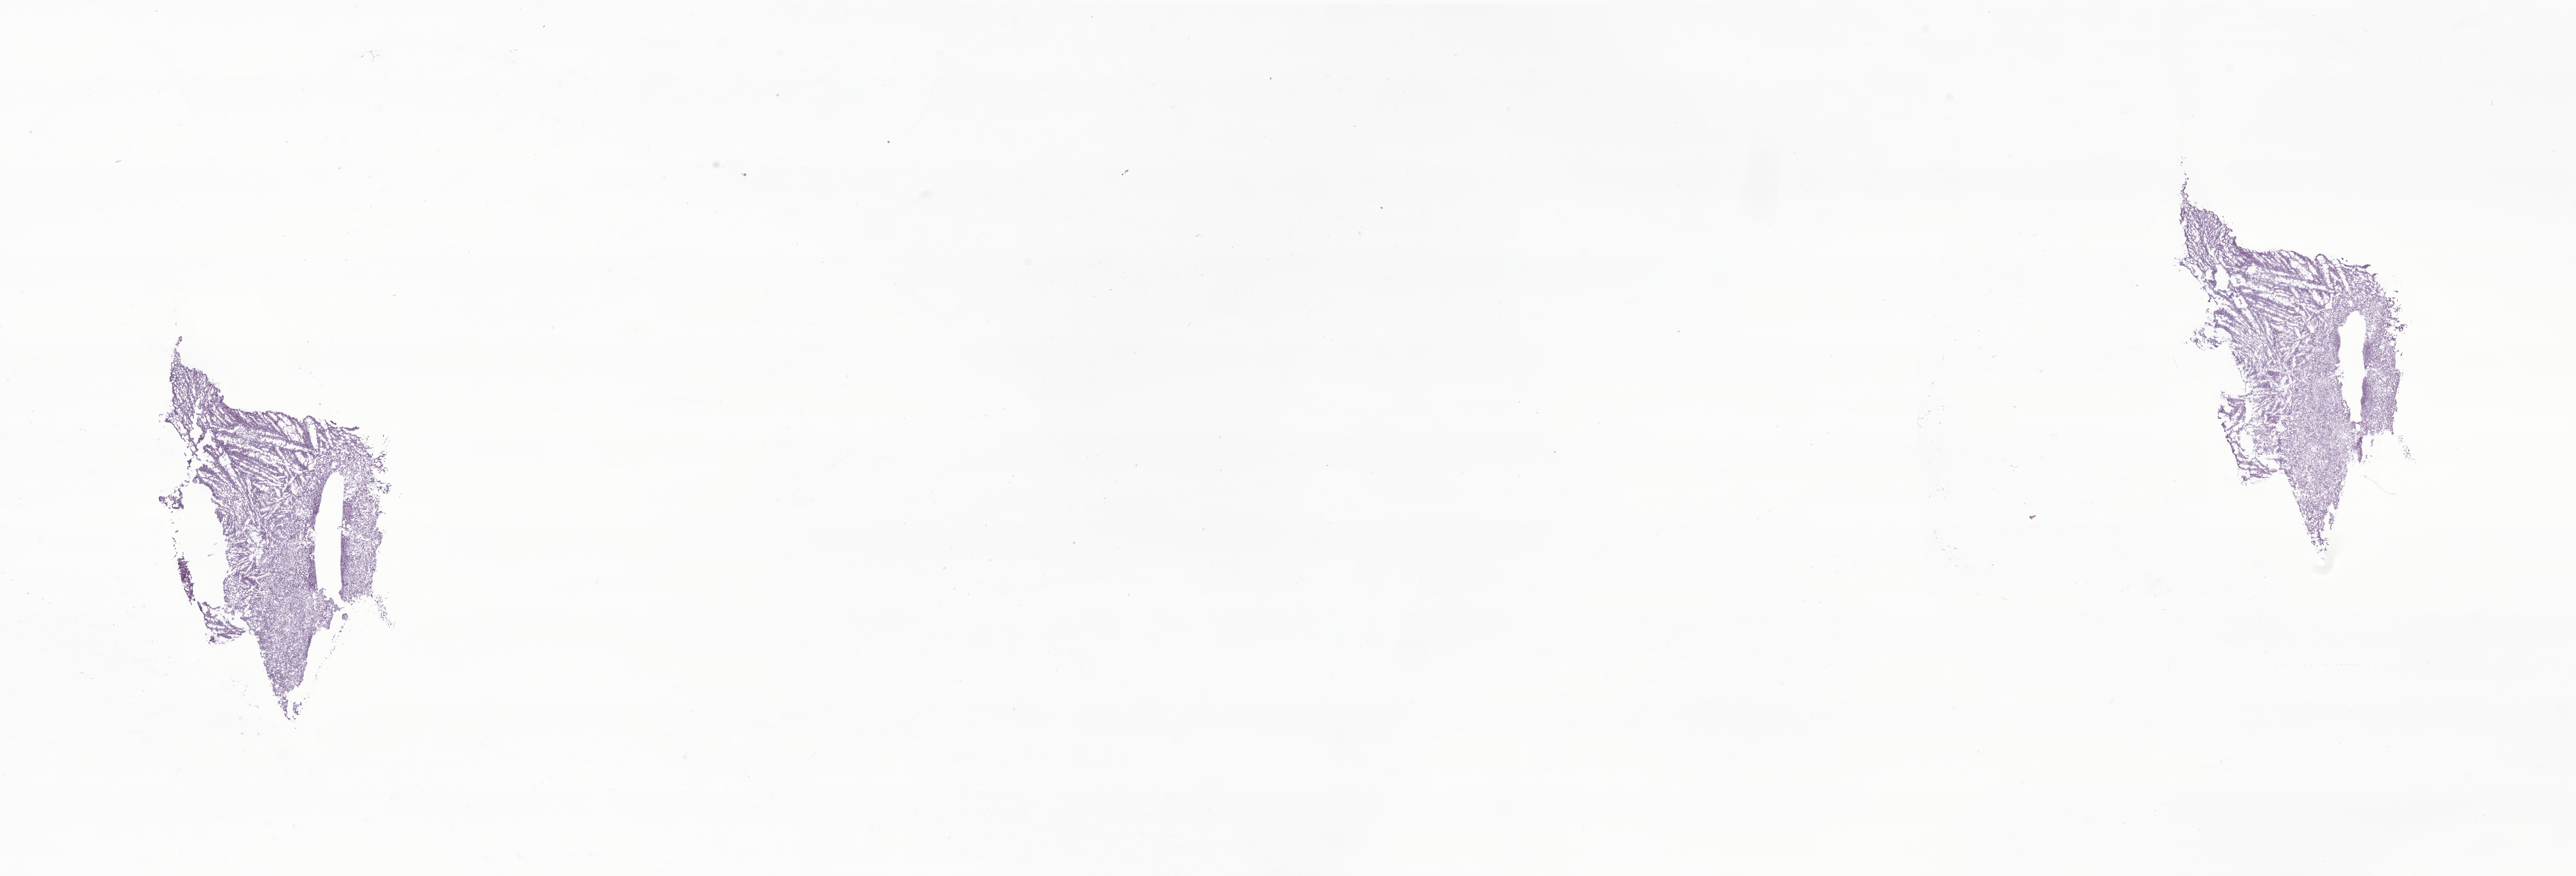
Whole-slide image, H&E stain of tumor tissue from the brain — a low-resolution overview of the entire scanned area, about 30.8 x 10.5 mm, frozen section (OCT-embedded). Female patient, age 241 months (20 years 1 month).
Diagnosis (ICD-O-3 morphology term): Medulloblastoma, NOS.